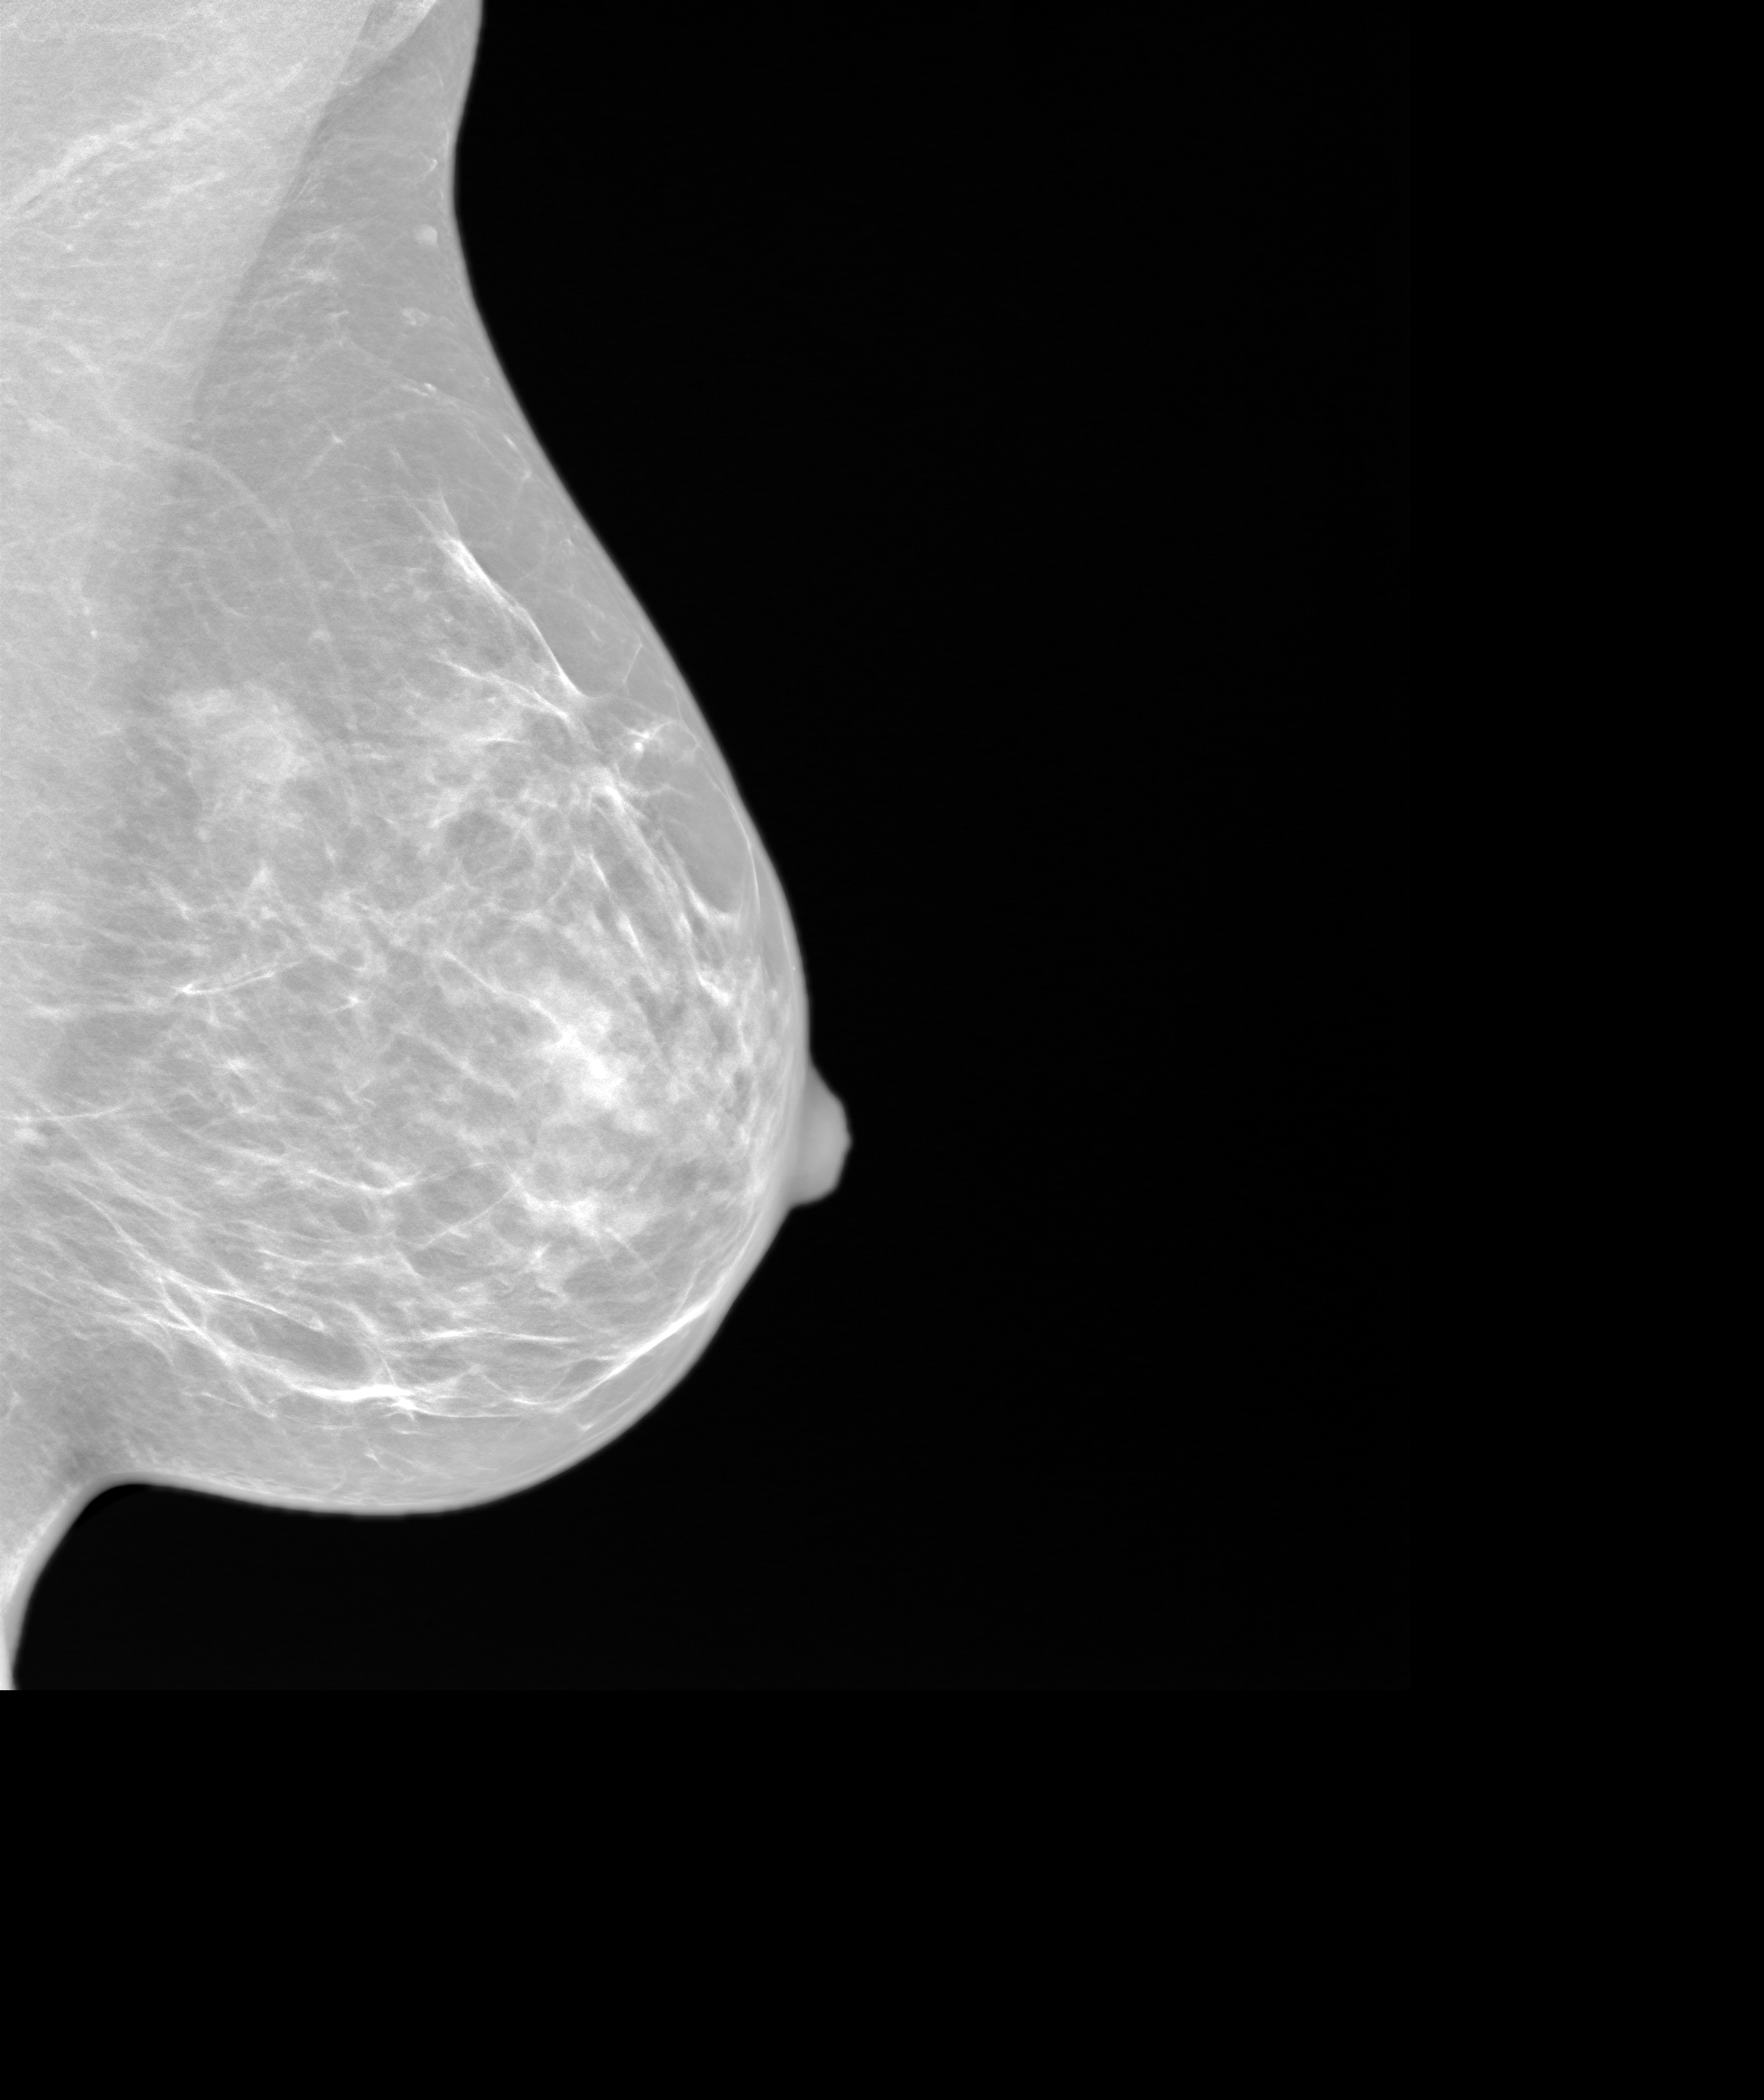
Annual screening mammography examination. Female patient, age 57 years.
Image type: synthesized 2-D view from tomosynthesis. Breast: left. Projection: MLO view.